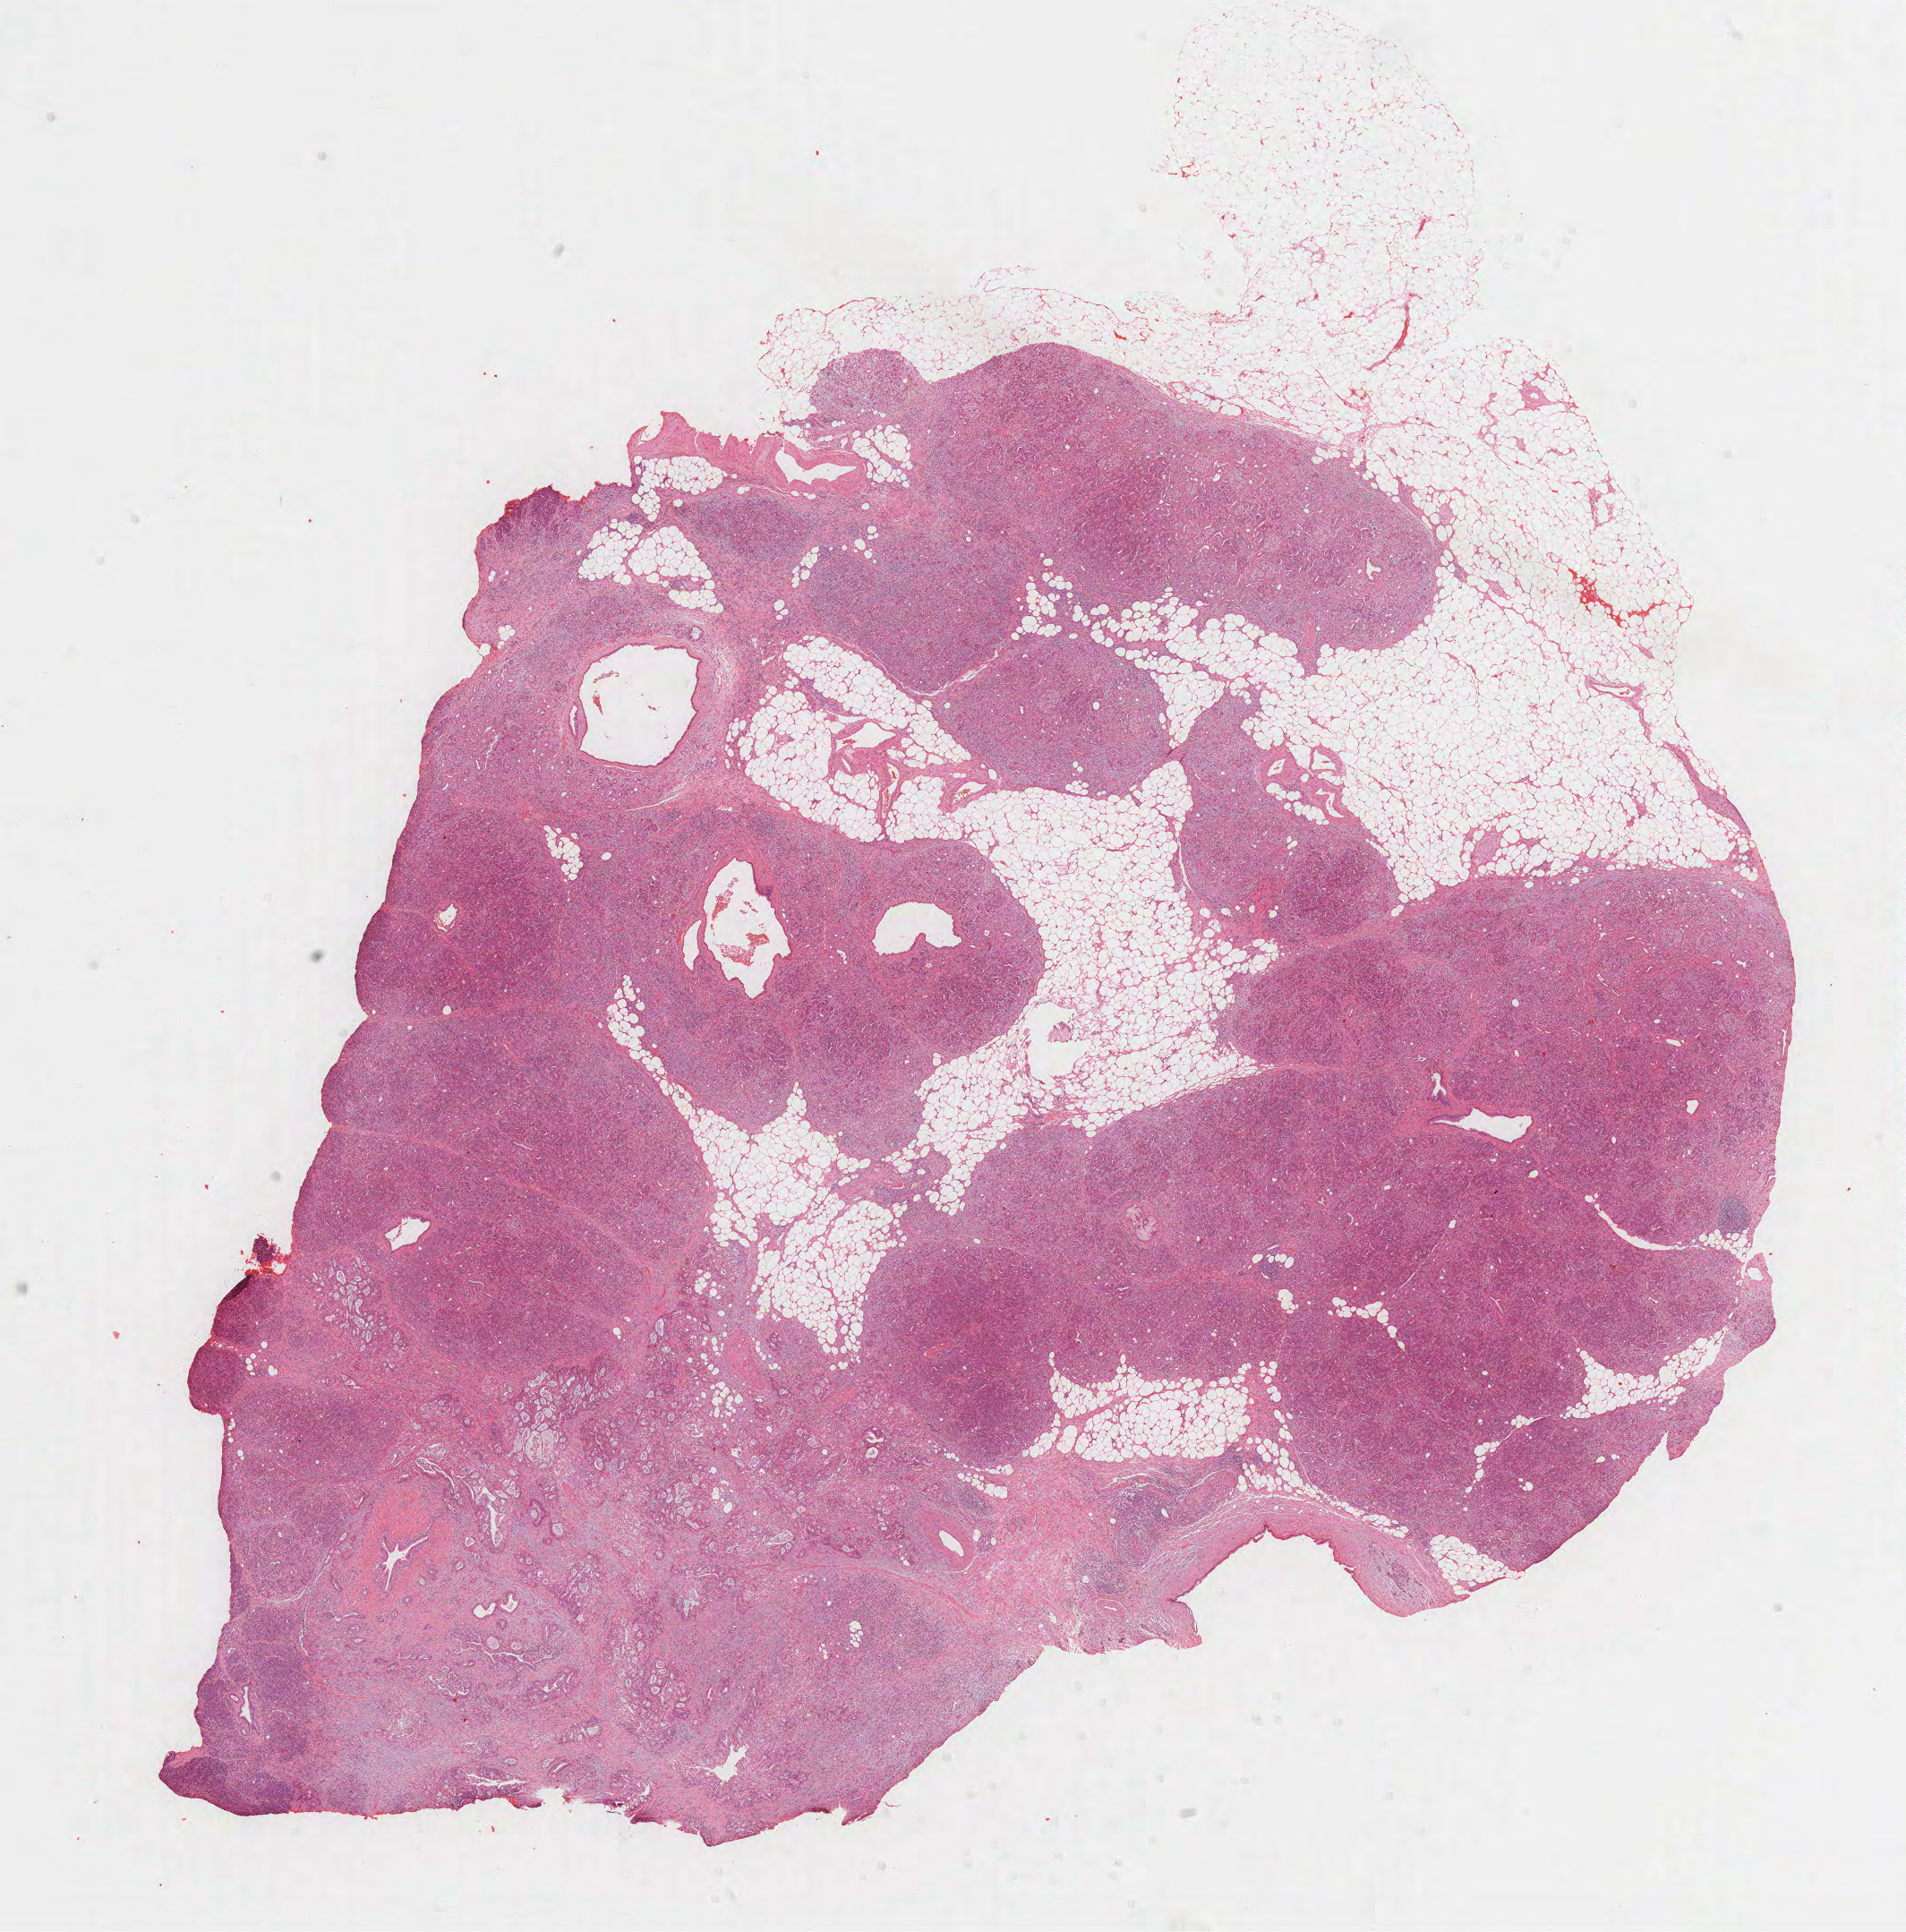
Digitized Hematoxylin and eosin (H&E) stained tissue section (whole slide) — a low-resolution overview of the entire scanned area, about 17.2 x 17.4 mm (slide scanned at 40x); formalin-fixed paraffin-embedded (FFPE) diagnostic section; primary tumour sample from the pancreas. Patient: male, age at initial diagnosis 67 years. Histologic grade: G2 (moderately differentiated).
• histologic diagnosis: Infiltrating duct carcinoma, NOS (head of pancreas)
• lymph nodes positive (case pathology): 0 of 23 examined
• AJCC pathologic stage: IIA (7th edition)